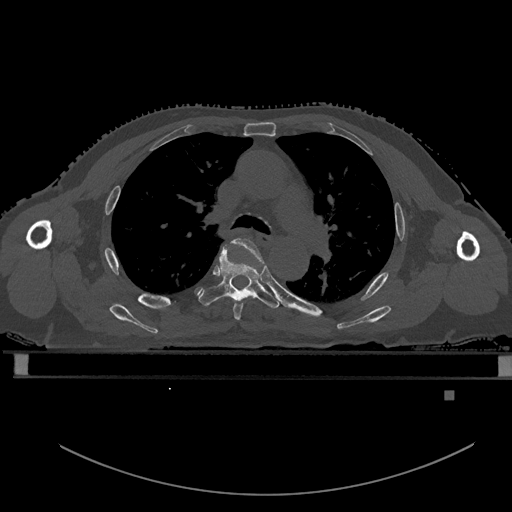
CT including the spine, one axial slice; position 373 of 969 along the scan axis; bone window (W 1800 / L 400 HU); 512 × 512 image matrix. Patient: male, 82 years. Case-level facts recorded for this patient, not image findings: primary cancer: prostate; vertebrae with lytic lesions (as recorded): T11, T9, T8, T2.
Outlined on this slice (semi-automatically segmented with operator editing):
- T4 vertebra: box from (x=233, y=238) to (x=263, y=321) px
- T5 vertebra: (x=199, y=246)–(x=280, y=309)